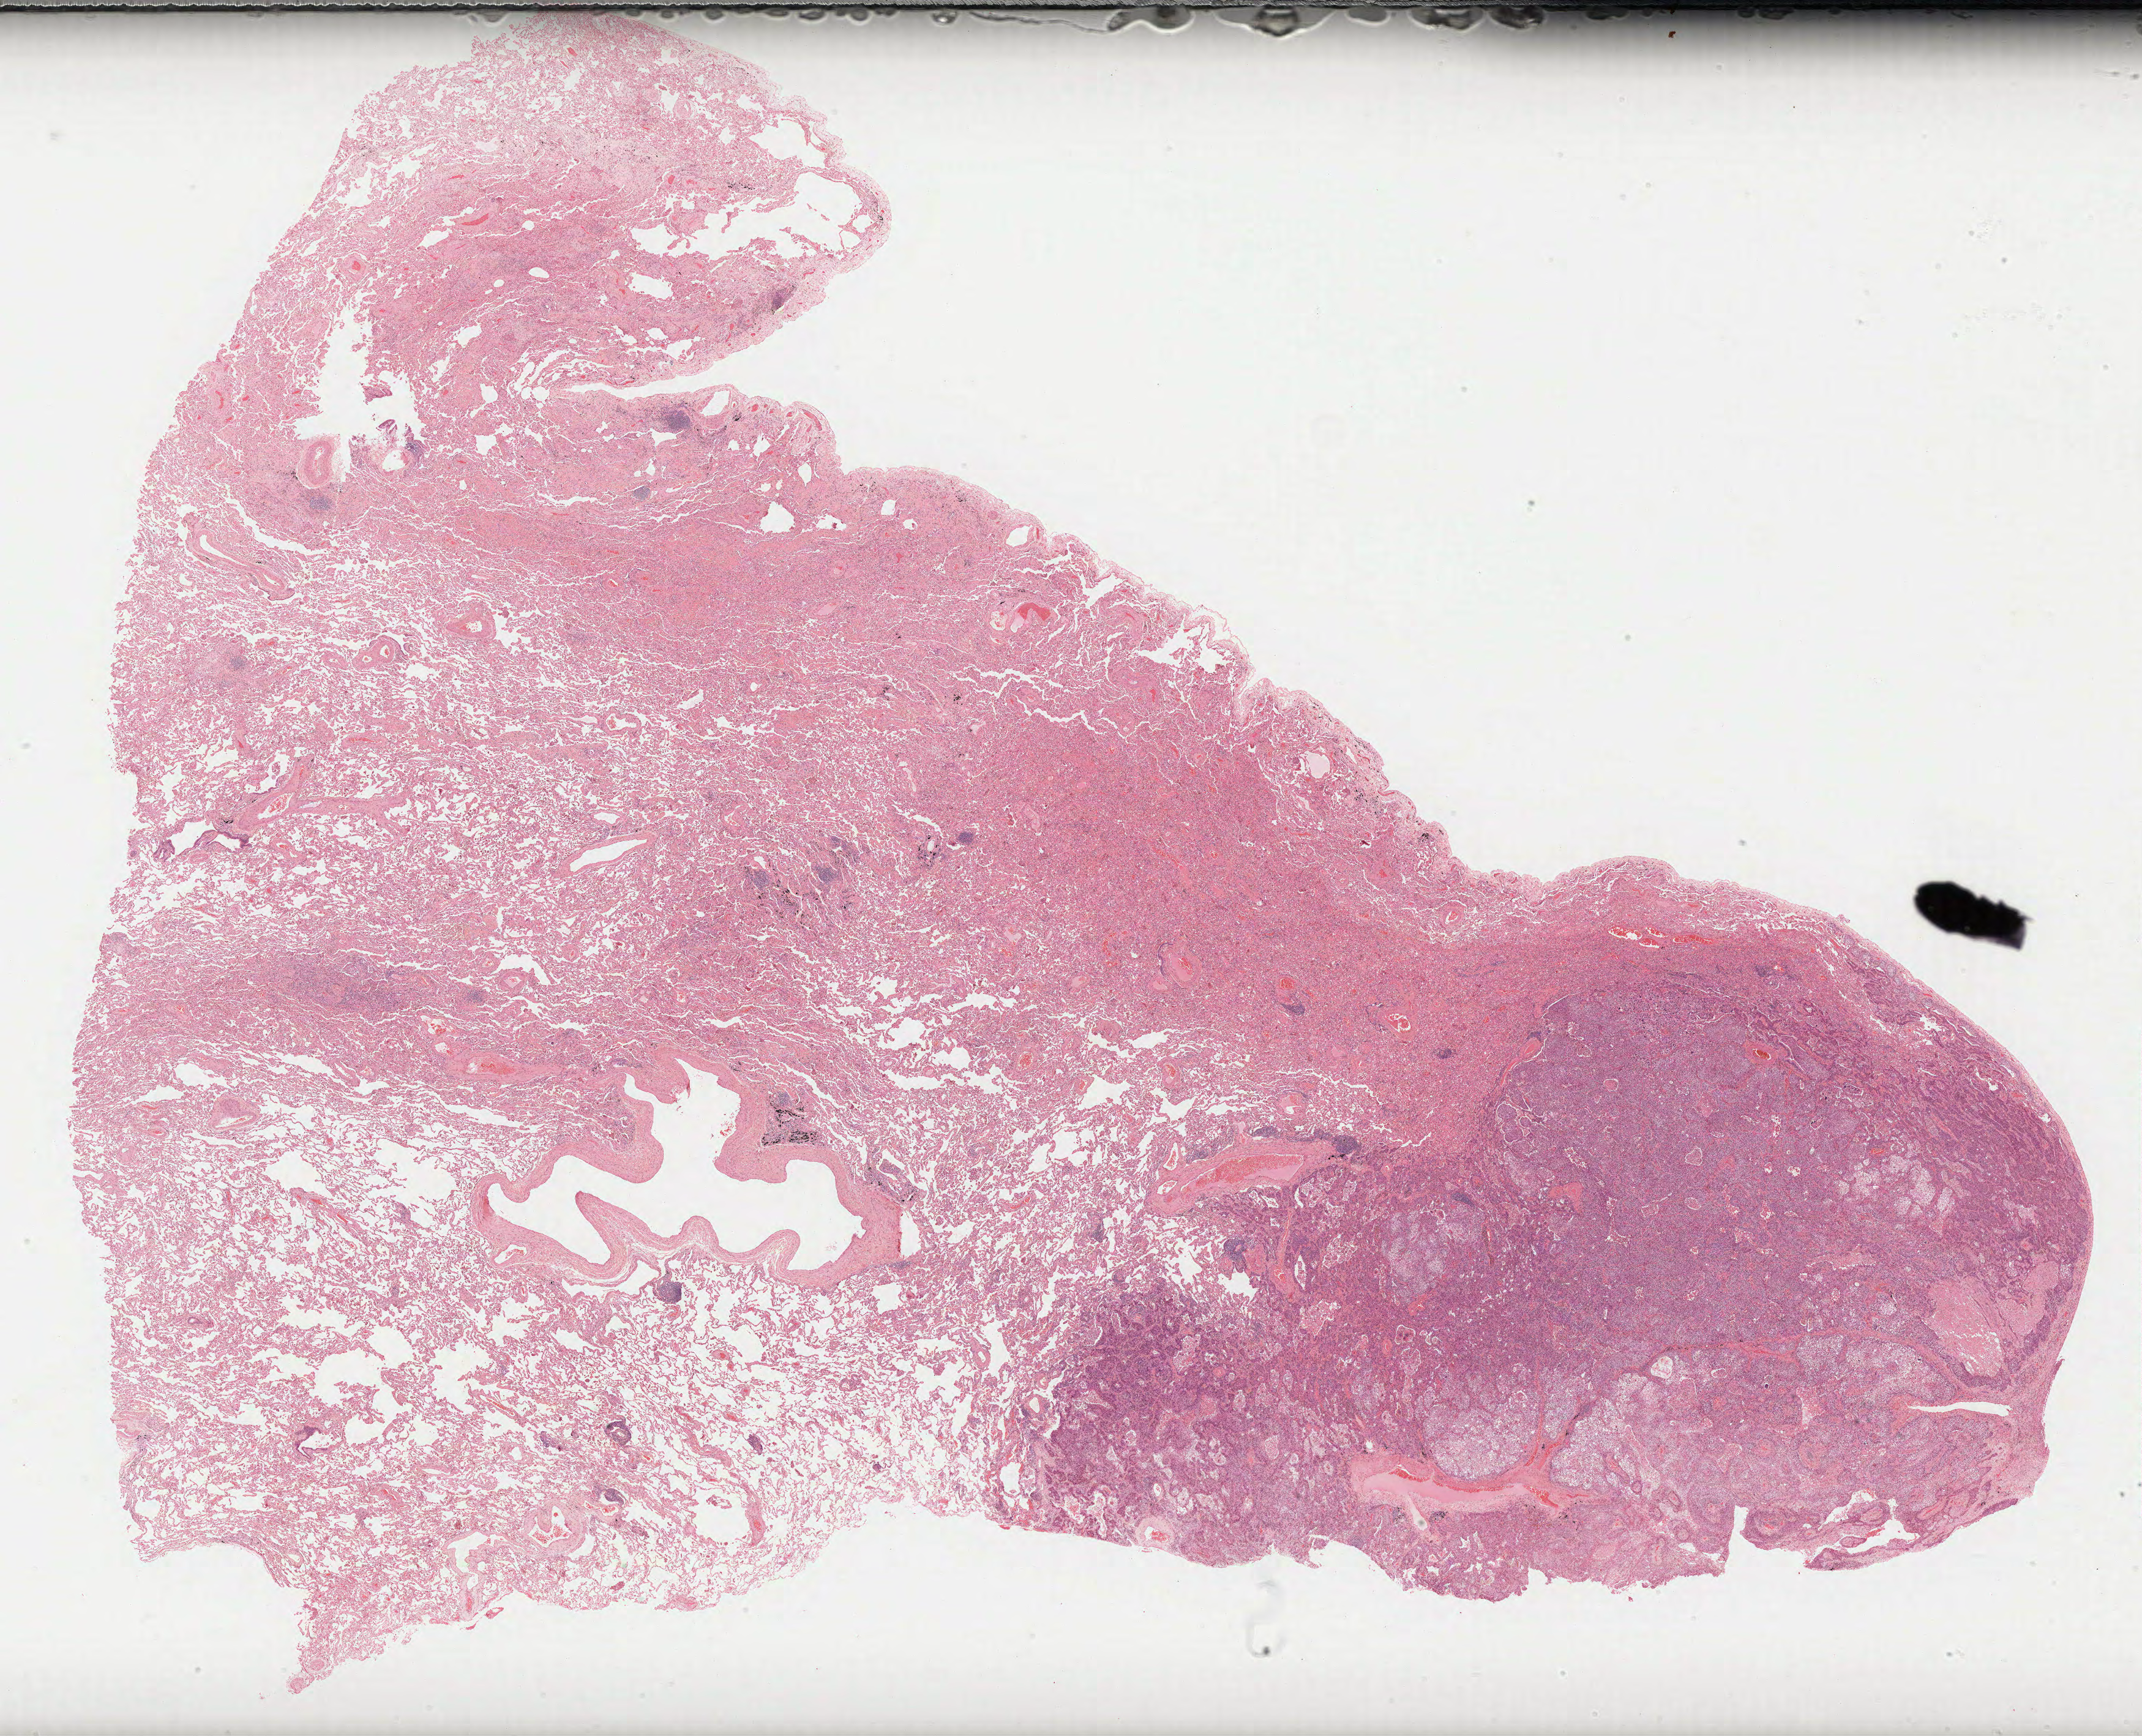
H&E whole-slide image, whole scanned area (about 28.2 x 22.9 mm, acquisition: 40x scan) shown as a low-resolution overview; formalin-fixed paraffin-embedded (FFPE) diagnostic section; lung, primary tumour sample. Patient: female, age at initial diagnosis 77 years.
• laterality: right
• pathologic diagnosis: Squamous cell carcinoma, NOS
• AJCC pathologic stage: IB